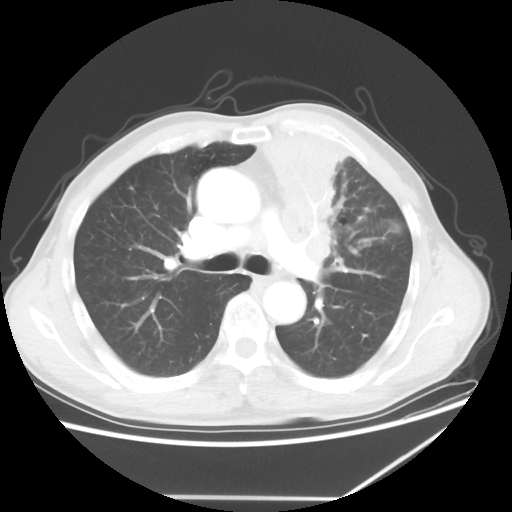
Chest CT, one axial slice. 100 kVp. Lung window (W 1500 / L -600 HU). 5 mm slice thickness. 512 × 512 image matrix, field of view 383 × 383 mm. Patient: male, 64 years. From the clinical record (not read from this slice): clinical TNM (as recorded): T1c N1 M1.
Outlined on this slice (rectangle marked by the reading radiologist):
- lung tumour (recorded histology: squamous cell carcinoma): bounding box [x1, y1, x2, y2] px = [242, 113, 363, 274]